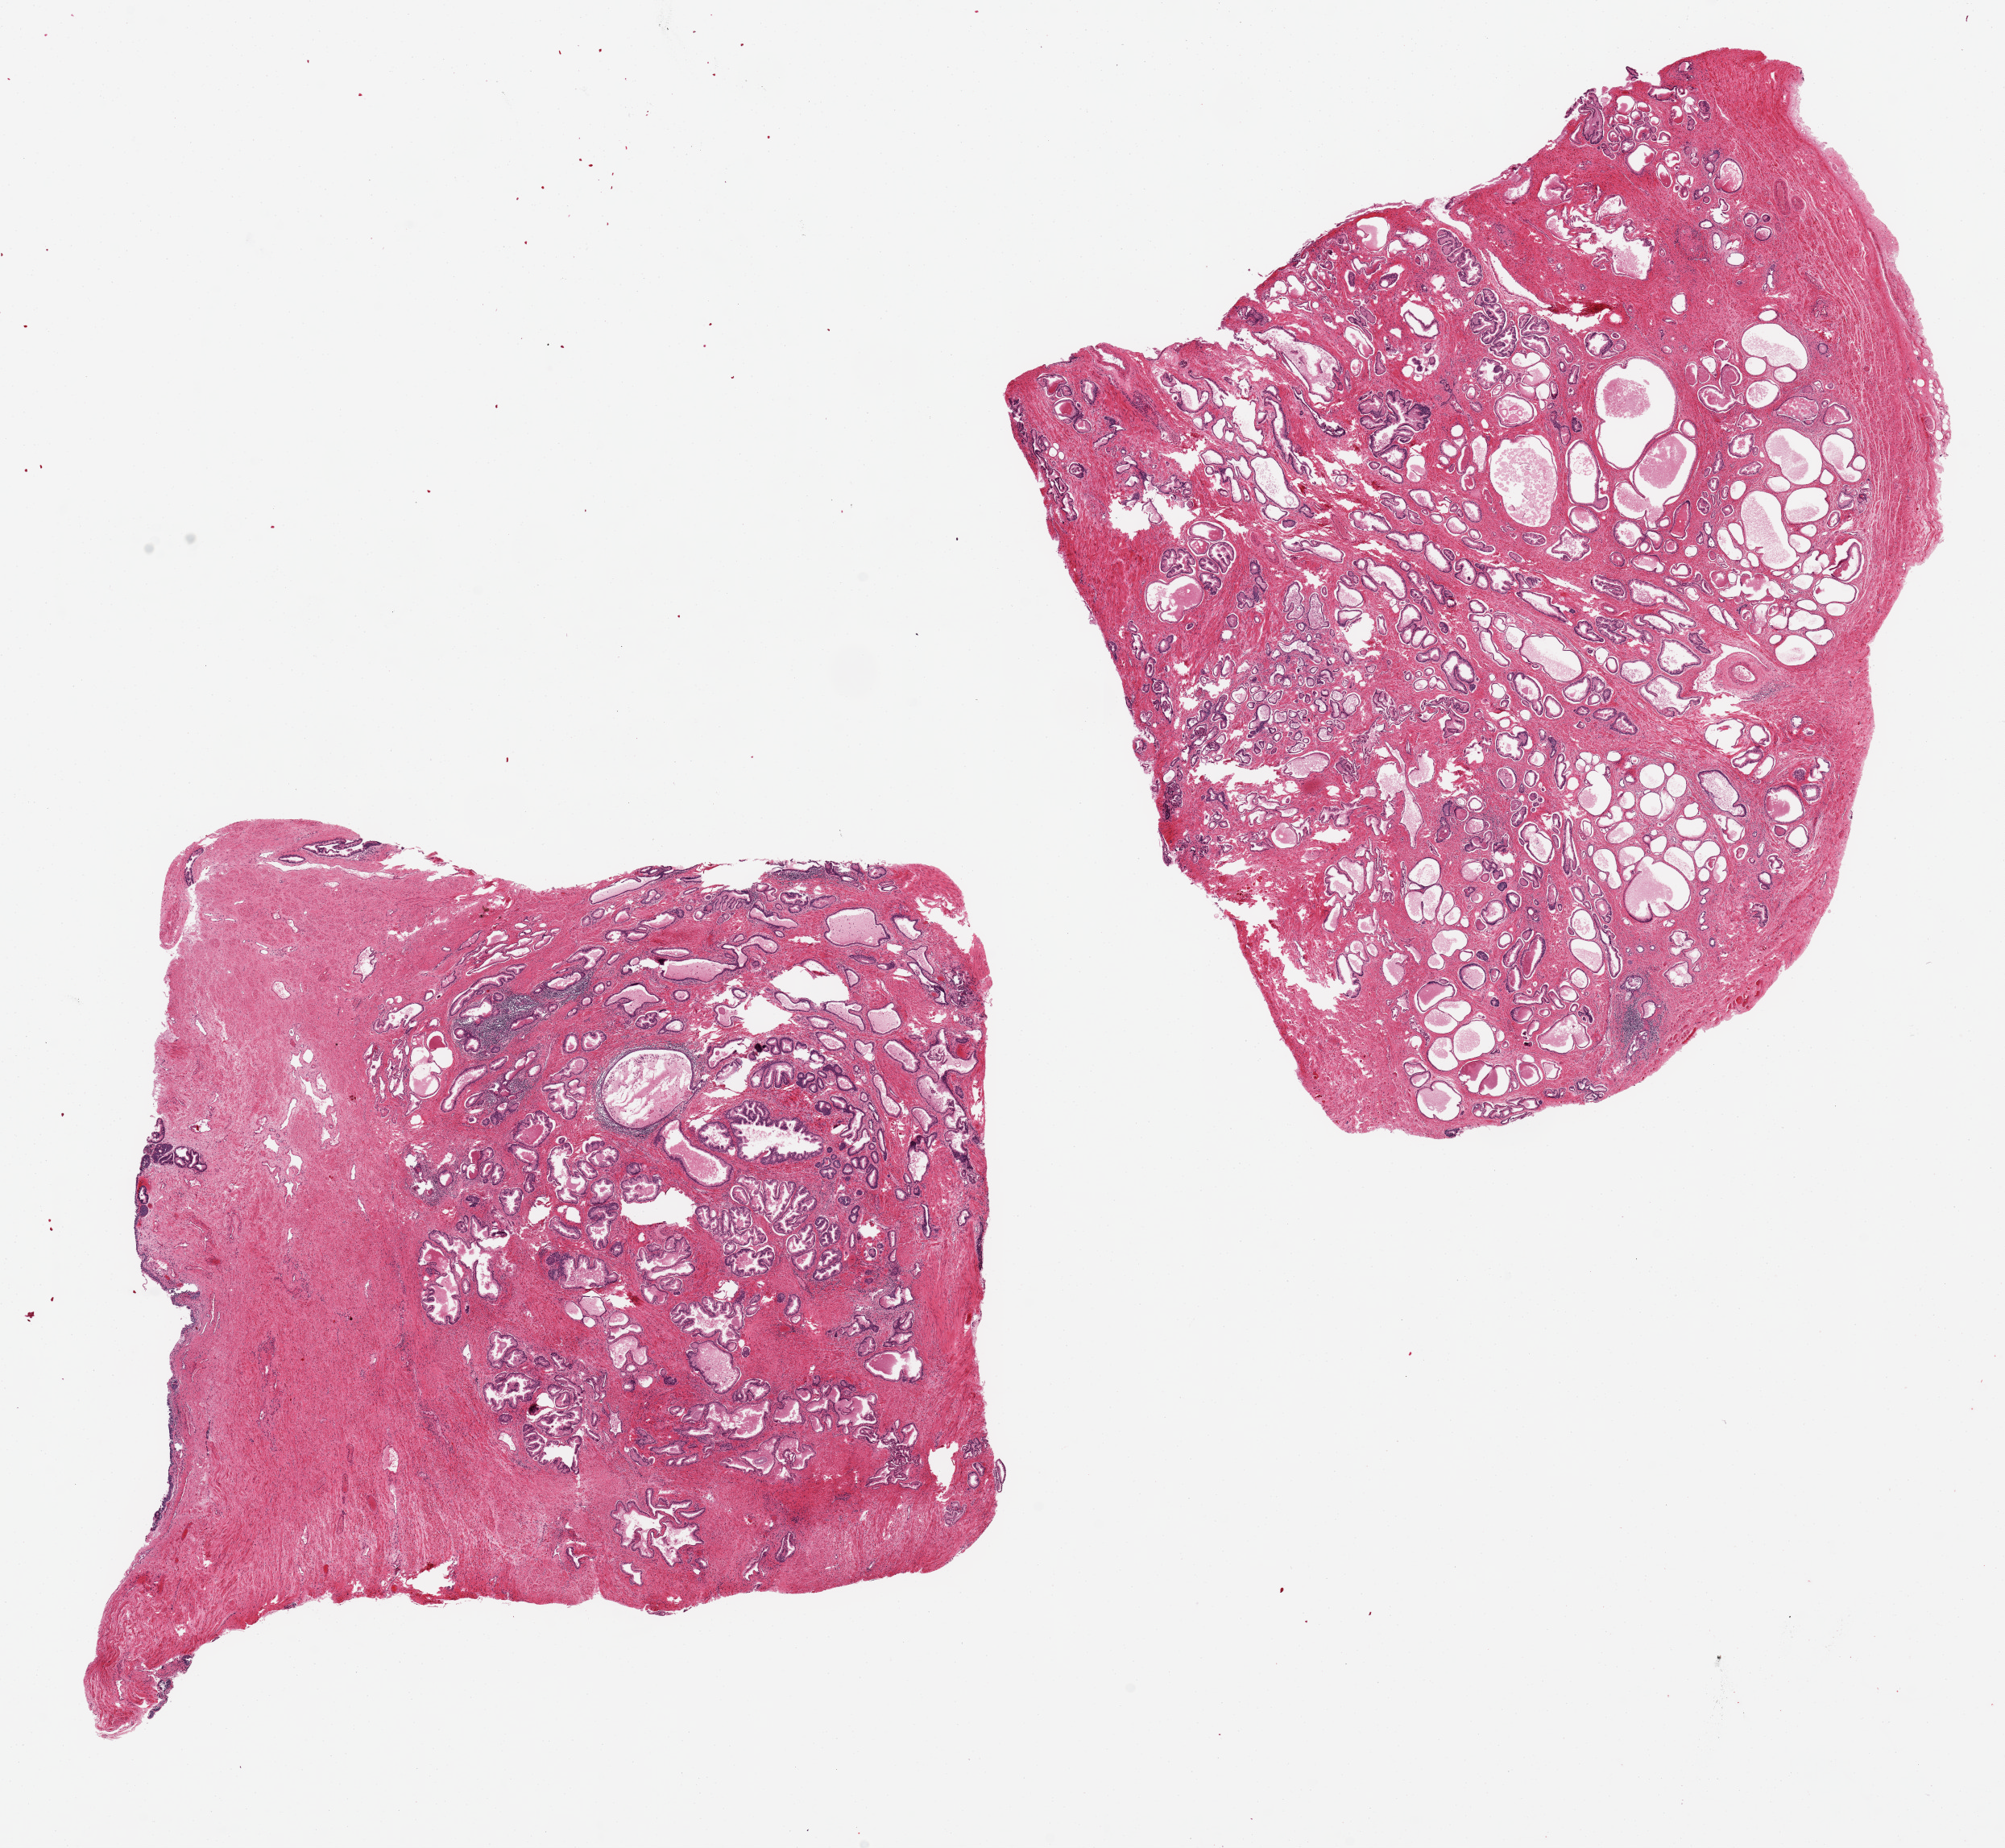
Digitized H&E-stained section — a low-resolution overview of the entire scanned area, about 19.7 x 18.1 mm (acquisition: 20x scan). PAXgene-fixed paraffin-embedded (PFPE) section. Target tissue: prostate. Donor tissue sample. Donor: male.
Review note (as recorded): 2 ~8x8mm aliquots. Prominent glandular hyperplasia; foci of cystic atrophy.